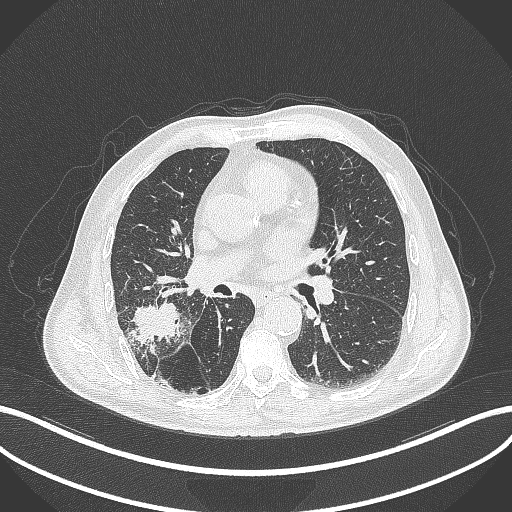
Chest CT, one axial slice. Slice 222 of 429 in the series (ordered by position). Lung window (W 1500 / L -600 HU). 1 mm slice thickness. 512 × 512 image matrix. Patient: male, 72 years. Case-level facts recorded for this patient, not image findings: clinical TNM (as recorded): T3 N2 M0.
Structures marked on this image (bounding box drawn by a radiologist):
- lung tumour (recorded histology: adenocarcinoma): bounding box (x1, y1, x2, y2) in pixels: (128, 300, 186, 351)